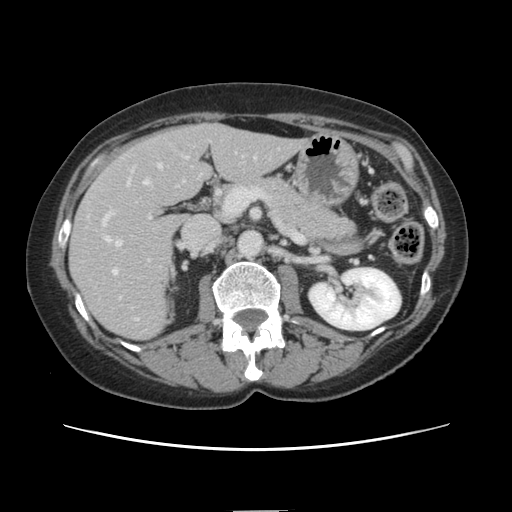
Contrast-enhanced abdominal CT, one axial slice. Intravenous contrast given. Soft-tissue window (W 400 / L 40 HU). 2.5 mm slice thickness. 512 × 512 image matrix, field of view 350 × 350 mm. Female patient, age 63 years. Case-level facts recorded for this patient, not image findings: diagnosis: colorectal cancer liver metastases, imaged before liver resection; multiple liver metastases: yes; largest metastasis: 3.2 cm; disease in both lobes: yes.
Structures marked on this image (expert manual segmentation):
- hepatic veins: bounding box (x1, y1, x2, y2) in pixels: (106, 164, 161, 276)
- liver: (71, 125, 303, 339)
- planned liver remnant (the part of the liver to remain after resection): (176, 125, 303, 190)
- portal vein (with intrahepatic branches): (102, 167, 146, 226)